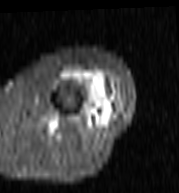
MRI of an extremity soft-tissue mass, one axial slice. STIR. MR volume resampled by the dataset authors to the PET/CT grid (not the native acquisition matrix). 3.27 mm slice thickness. 179 × 193 image matrix. Female patient. Case-level facts recorded for this patient, not image findings: histological type: undifferentiated – high grade; grade: high; site of the primary tumour: left thigh.
Structures marked on this image (expert contour drawn on MRI and transferred to this co-registered scan by the dataset authors):
- gross tumour volume including surrounding oedema: bounding box [x1, y1, x2, y2] px = [63, 67, 119, 116]